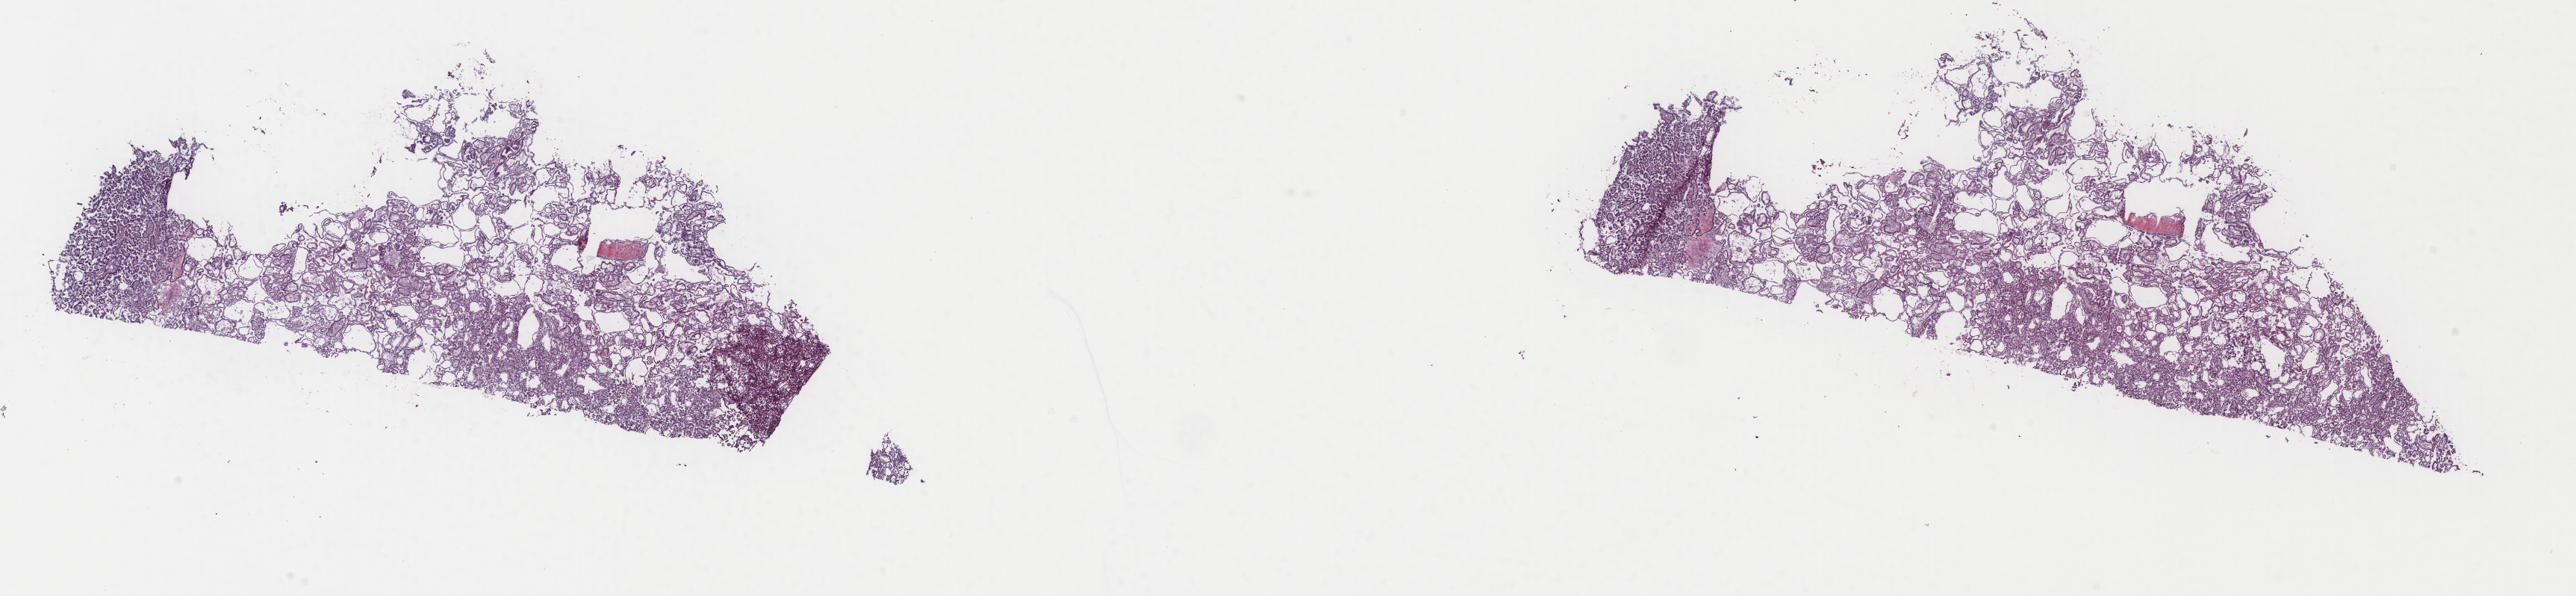
Digitized H&E-stained tissue section (whole slide) — a low-resolution overview of the entire scanned area, about 27.4 x 6.3 mm (from a 40x scan); frozen section from the top of the tissue portion; kidney, primary tumour sample. Male patient; age at initial diagnosis 47 years. Pathologist review of this section (percent, as recorded): tumour cells 100%, tumour nuclei 75%, normal cells 0%, stromal cells 0%, necrosis 0%. Inflammatory infiltration, as recorded: lymphocyte infiltration 3%, monocyte infiltration 2%, neutrophil infiltration 0%.
• pathologic diagnosis: Papillary adenocarcinoma, NOS
• AJCC pathologic stage: I (7th edition)